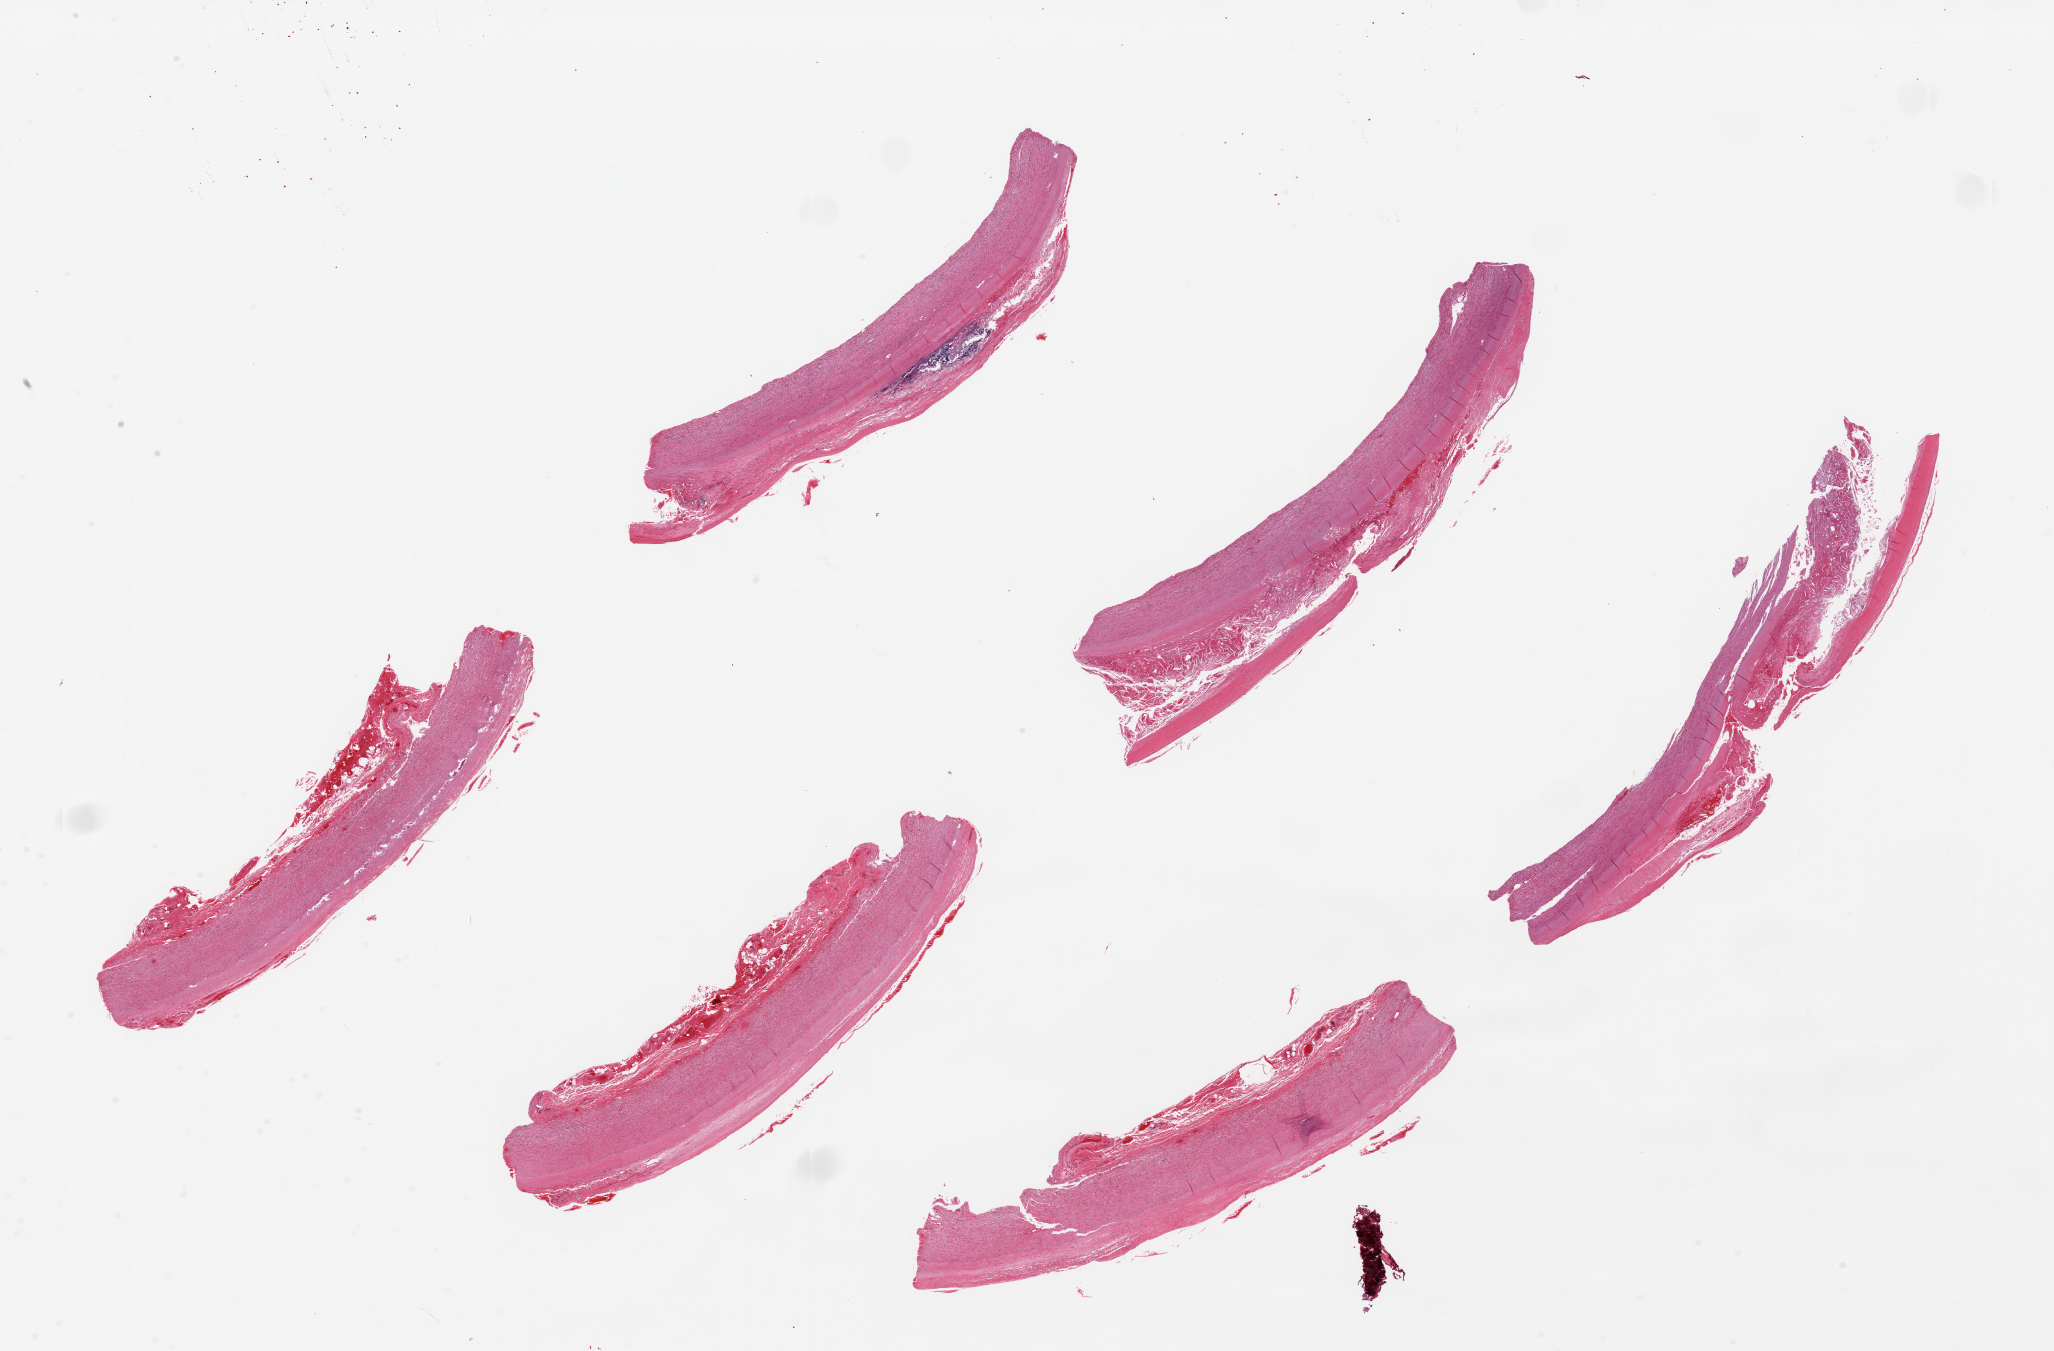
H&E whole-slide image, brightfield — low-resolution overview of the scanned area, about 32.5 x 21.4 mm (acquisition: 20x scan); PAXgene-fixed paraffin-embedded (PFPE) section; sampled site (target tissue): aorta; tissue donor sample. Male donor.
Review note (as recorded): 6 pieces, ~9x2mm.